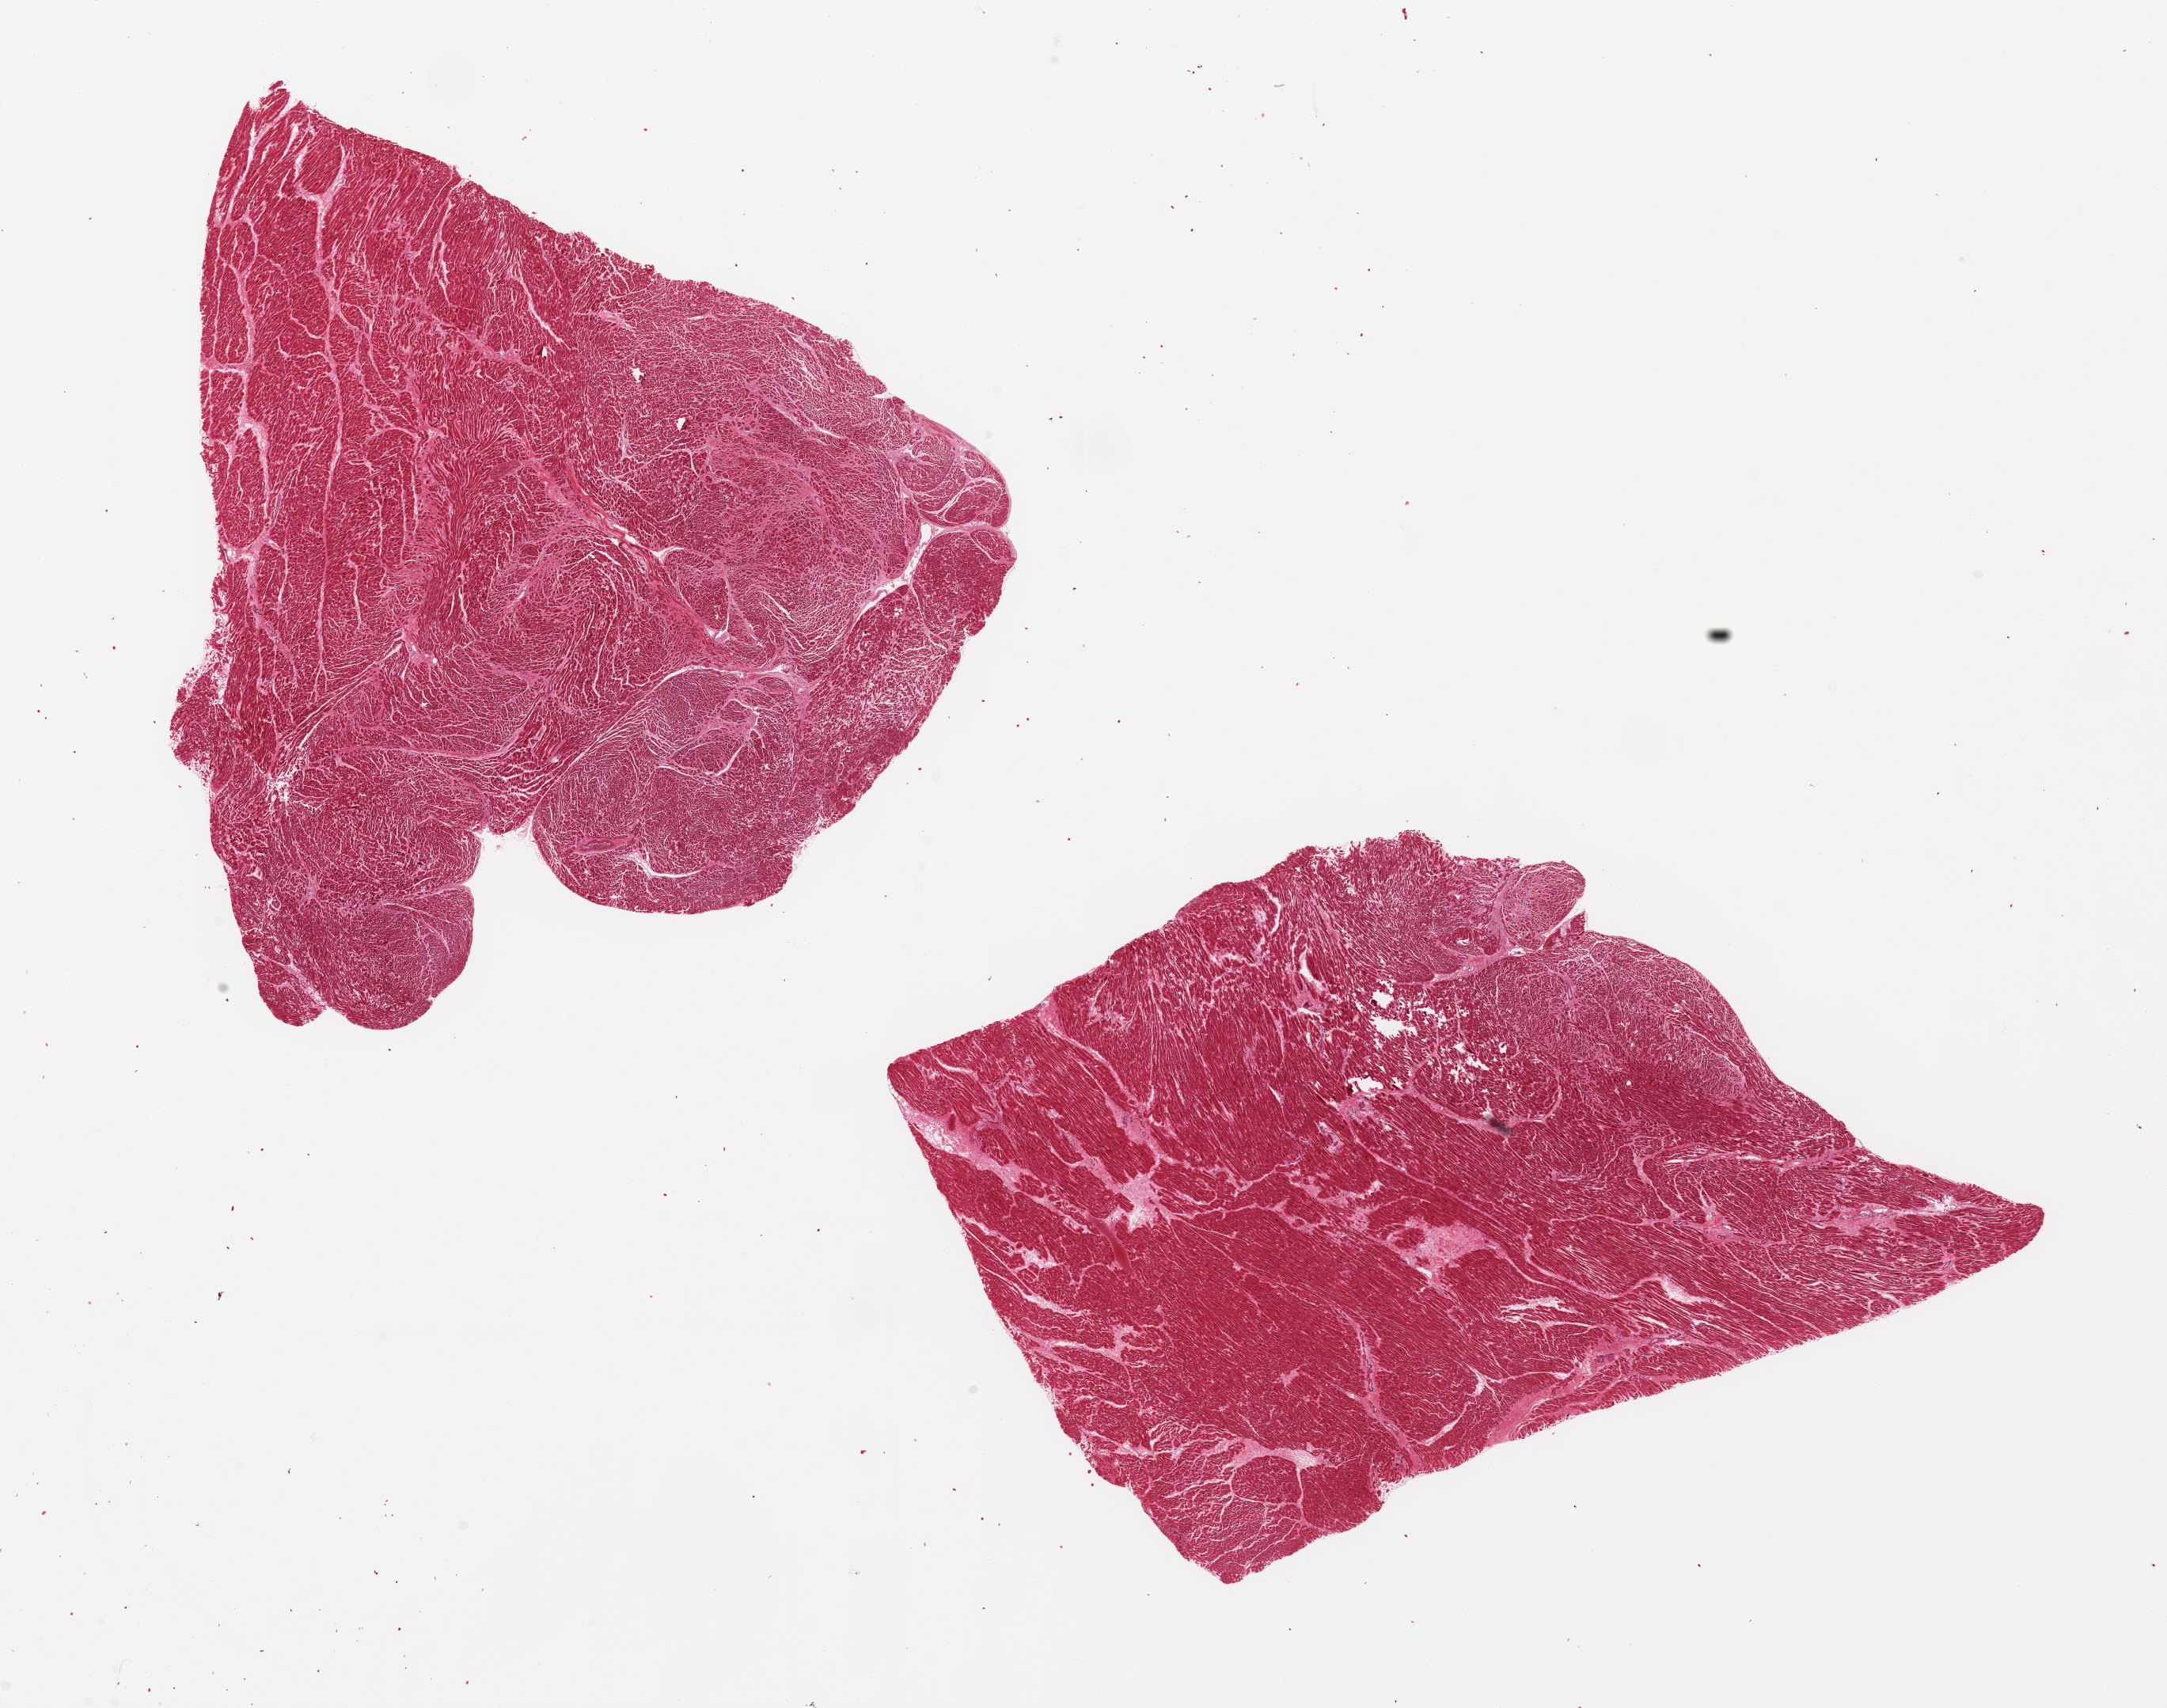
Digitized hematoxylin and eosin (H&E)-stained section, low-resolution overview of the scanned area, about 21.7 x 17.1 mm (acquisition: 20x scan). PAXgene-fixed paraffin-embedded (PFPE) section. Target tissue: heart. Donor tissue sample.
Reviewer comment on this tissue sample: 2 pieces ~8mm. foci of patchy fibrosis c/w infarcts.